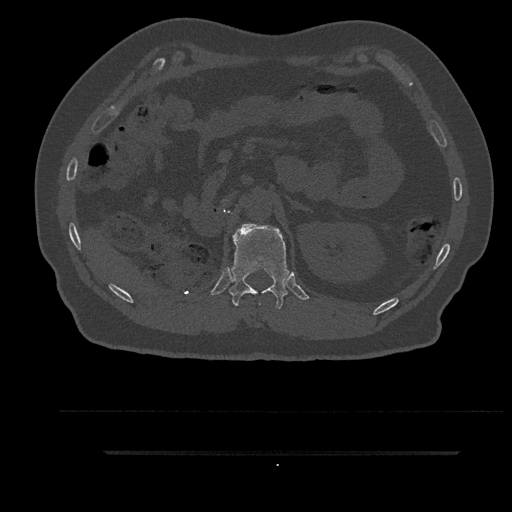
CT including the spine, one axial slice; slice 242 of 797 in the series (ordered by position); 120 kVp; bone window (W 1800 / L 400 HU); 512 × 512 image matrix. Male patient, age 63 years. Case-level facts recorded for this patient, not image findings: primary cancer: renal.
Outlined on this slice (semi-automatic segmentation, software-assisted and operator-edited):
- T12 vertebra: bounding box (x1, y1, x2, y2) in pixels: (229, 224, 289, 309)